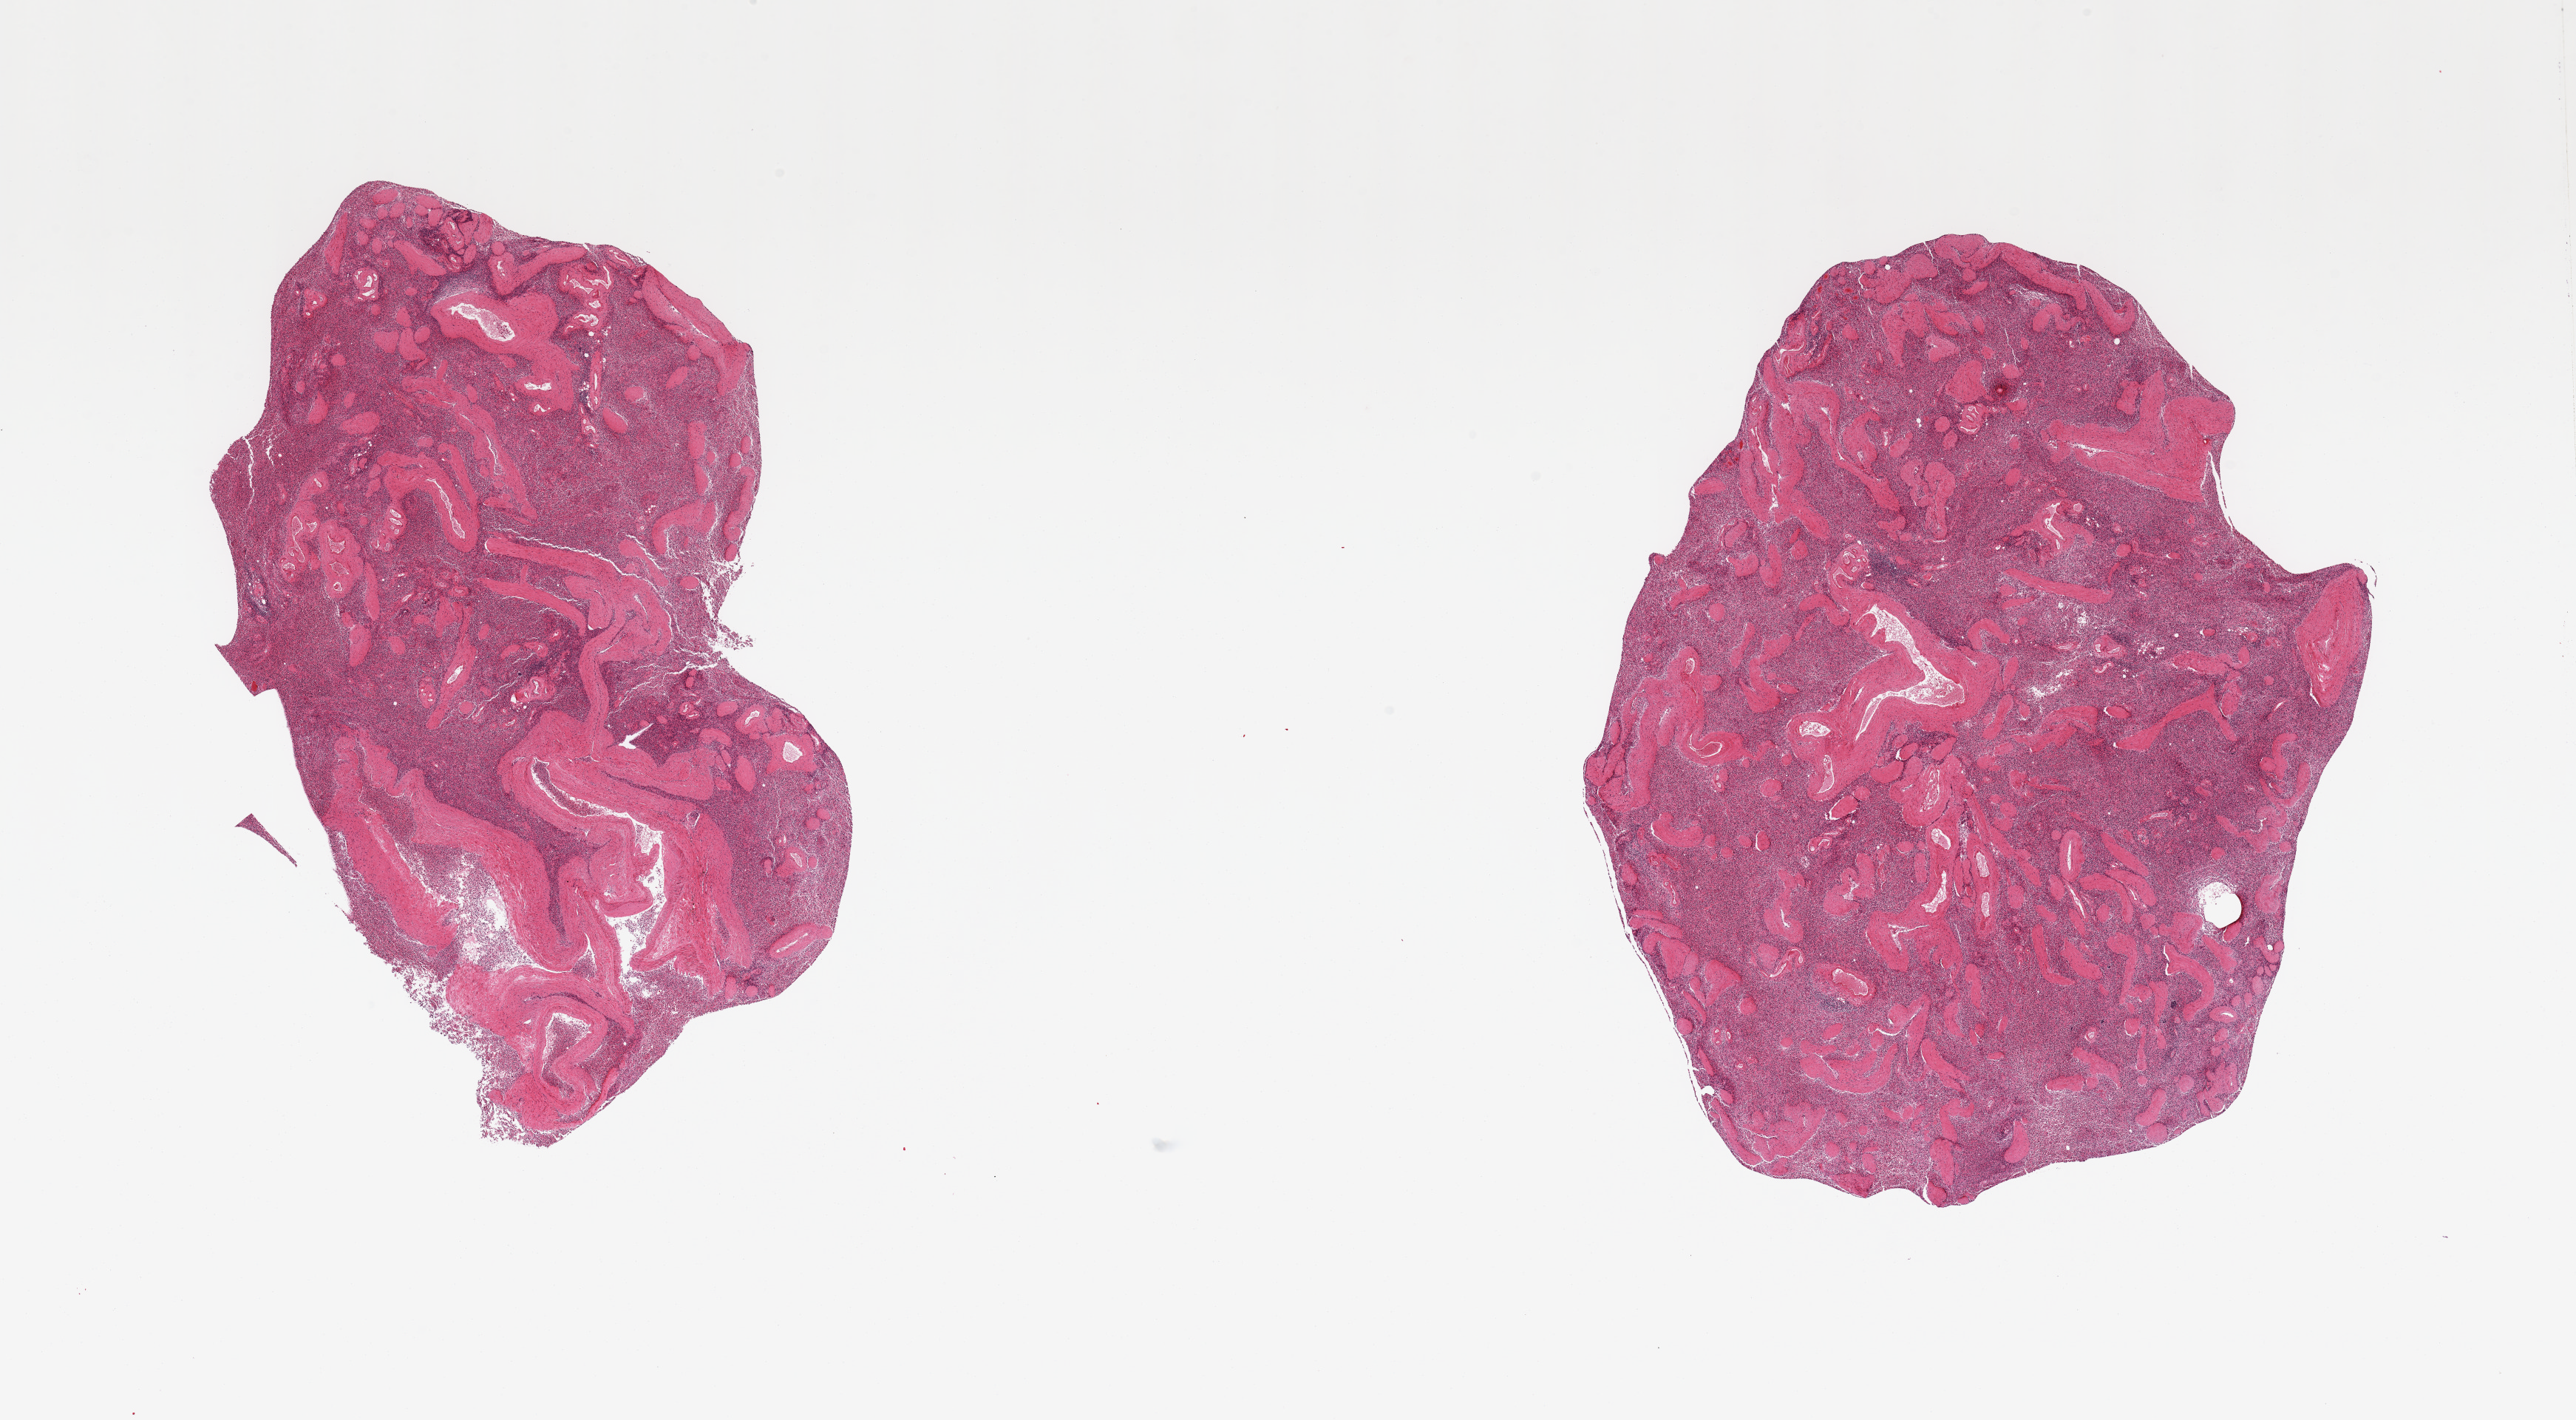
Digitized hematoxylin and eosin (H&E)-stained section — a low-resolution overview of the entire scanned area, about 27.6 x 15.2 mm. PAXgene-fixed paraffin-embedded (PFPE) section. Section of spleen (target tissue). Tissue donor sample.
Reviewer comment on this tissue sample: 2 pieces.